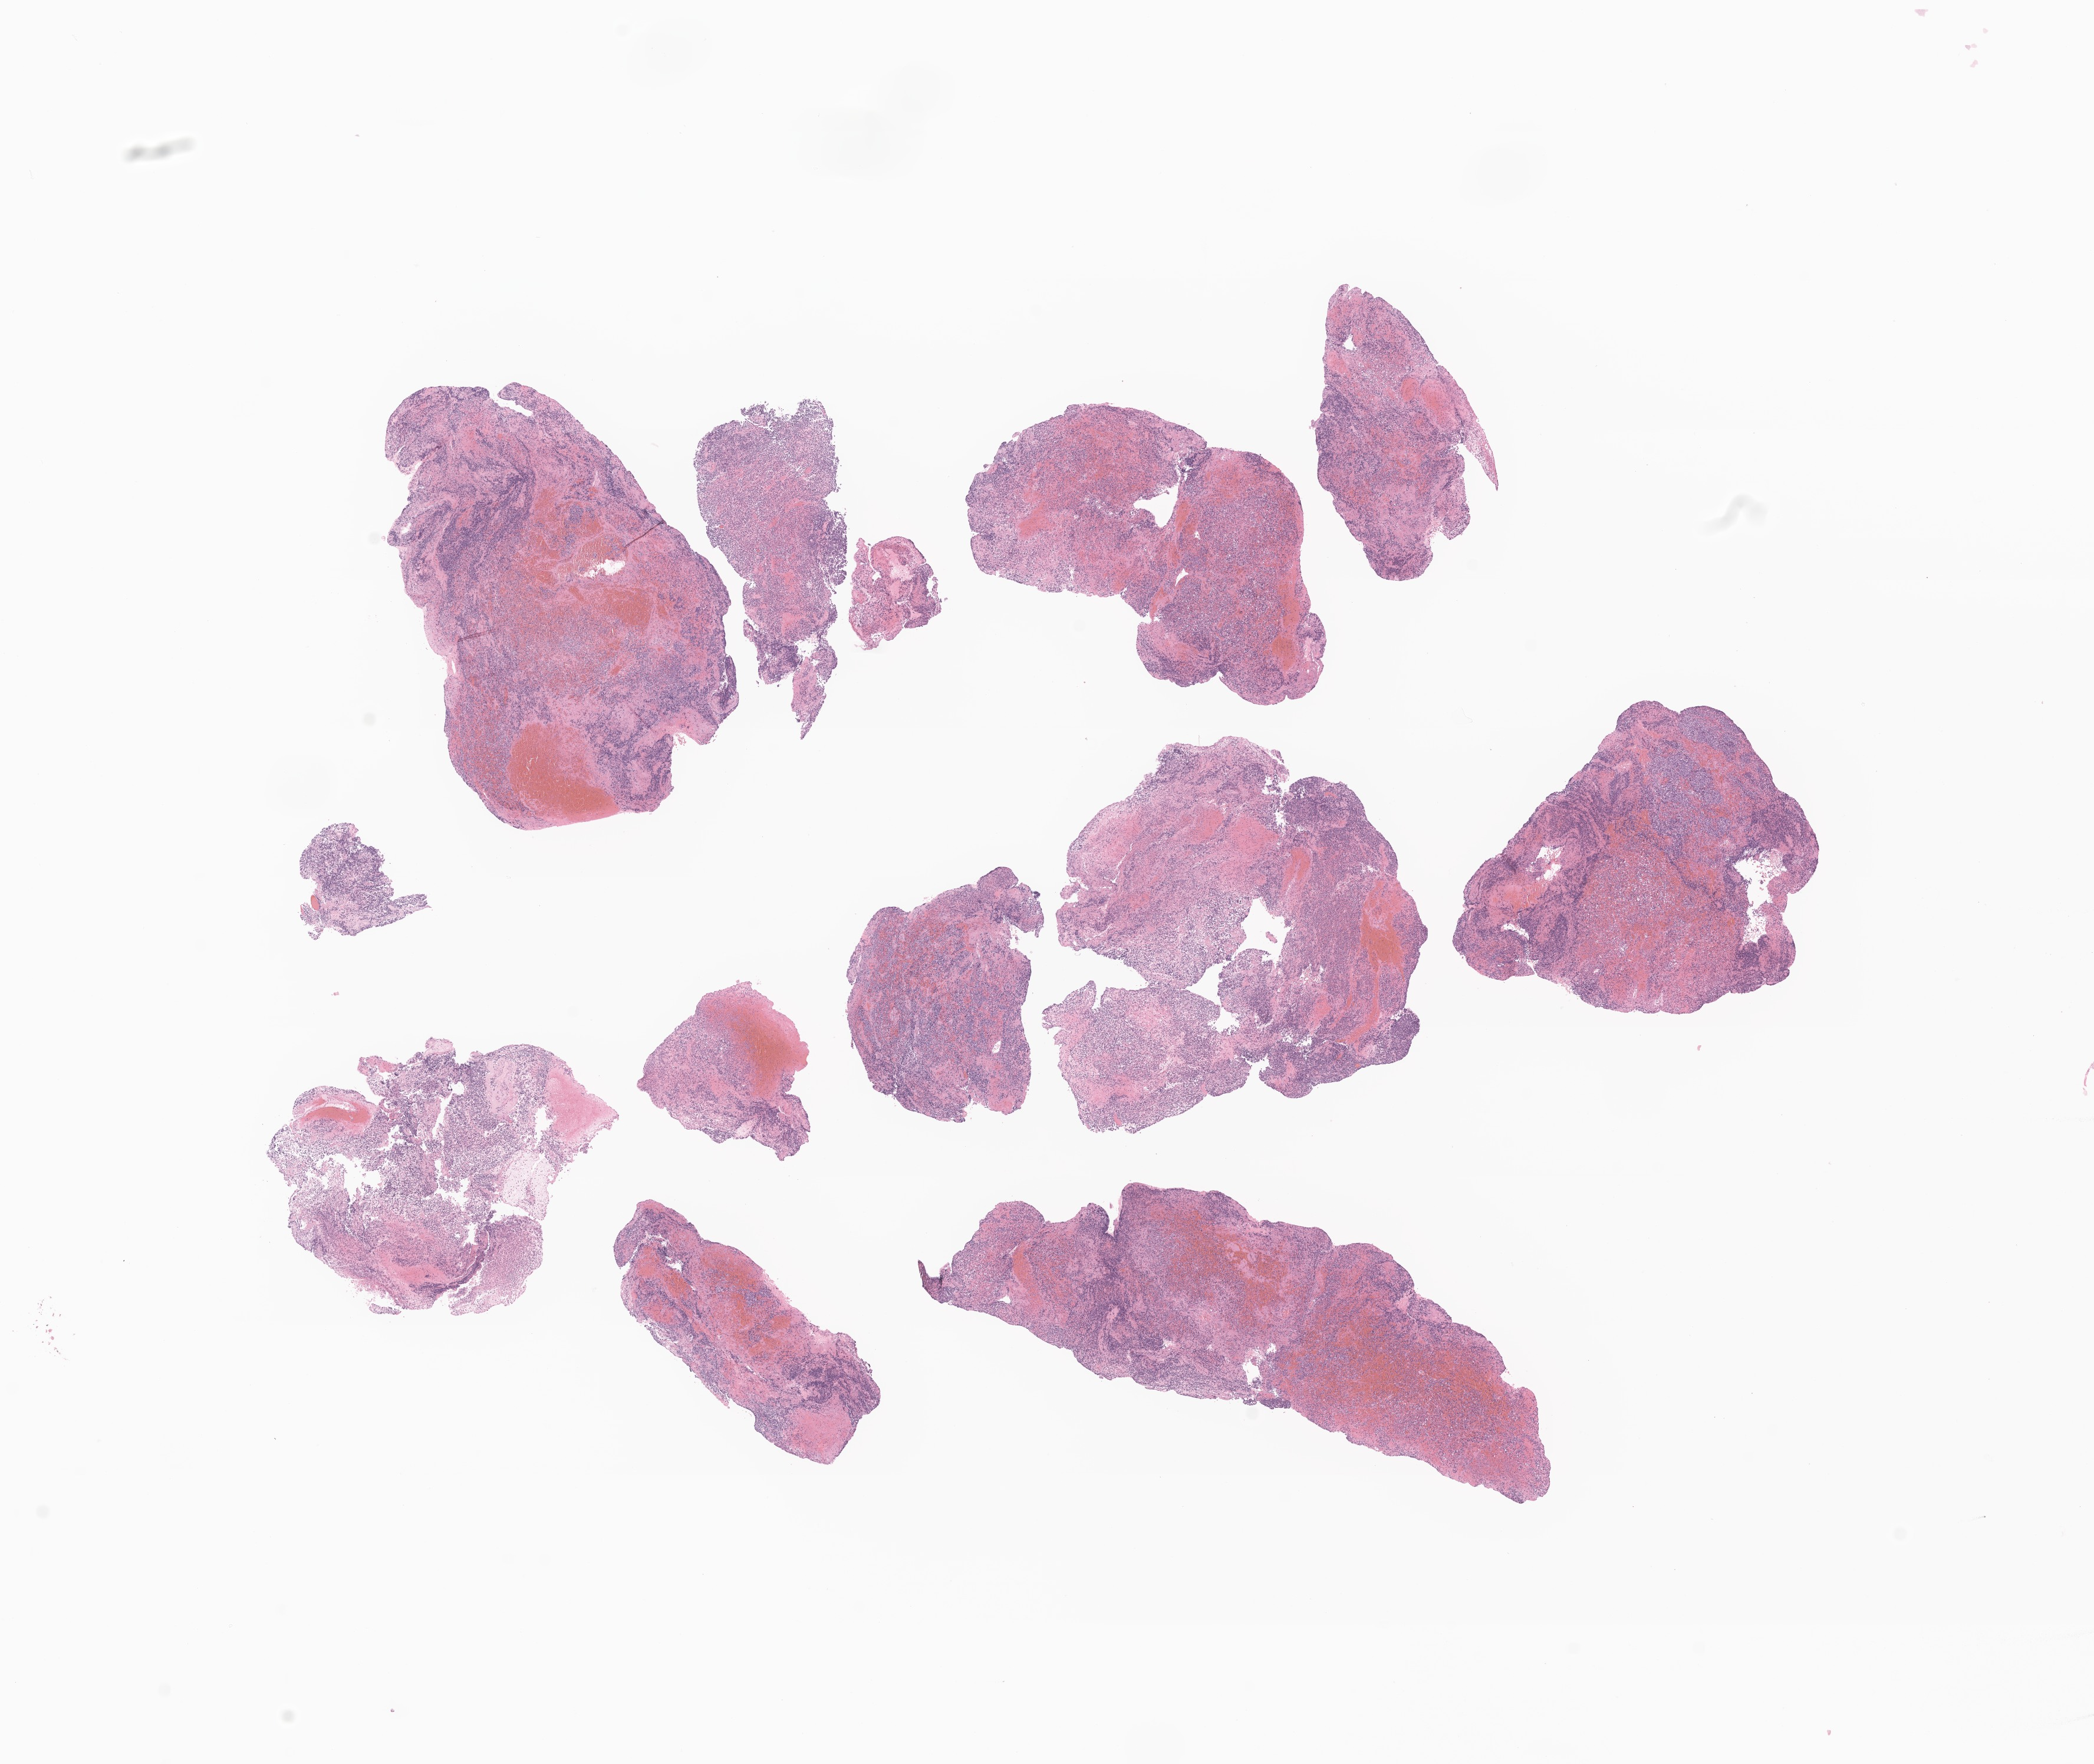
H&E whole-slide image of tumor tissue from the brain — whole scanned area (about 15.0 x 12.6 mm) shown as a low-resolution overview, formalin-fixed paraffin-embedded section. Patient male; age 195 months (16 years 3 months).
Recorded diagnosis: Medulloblastoma, NOS.